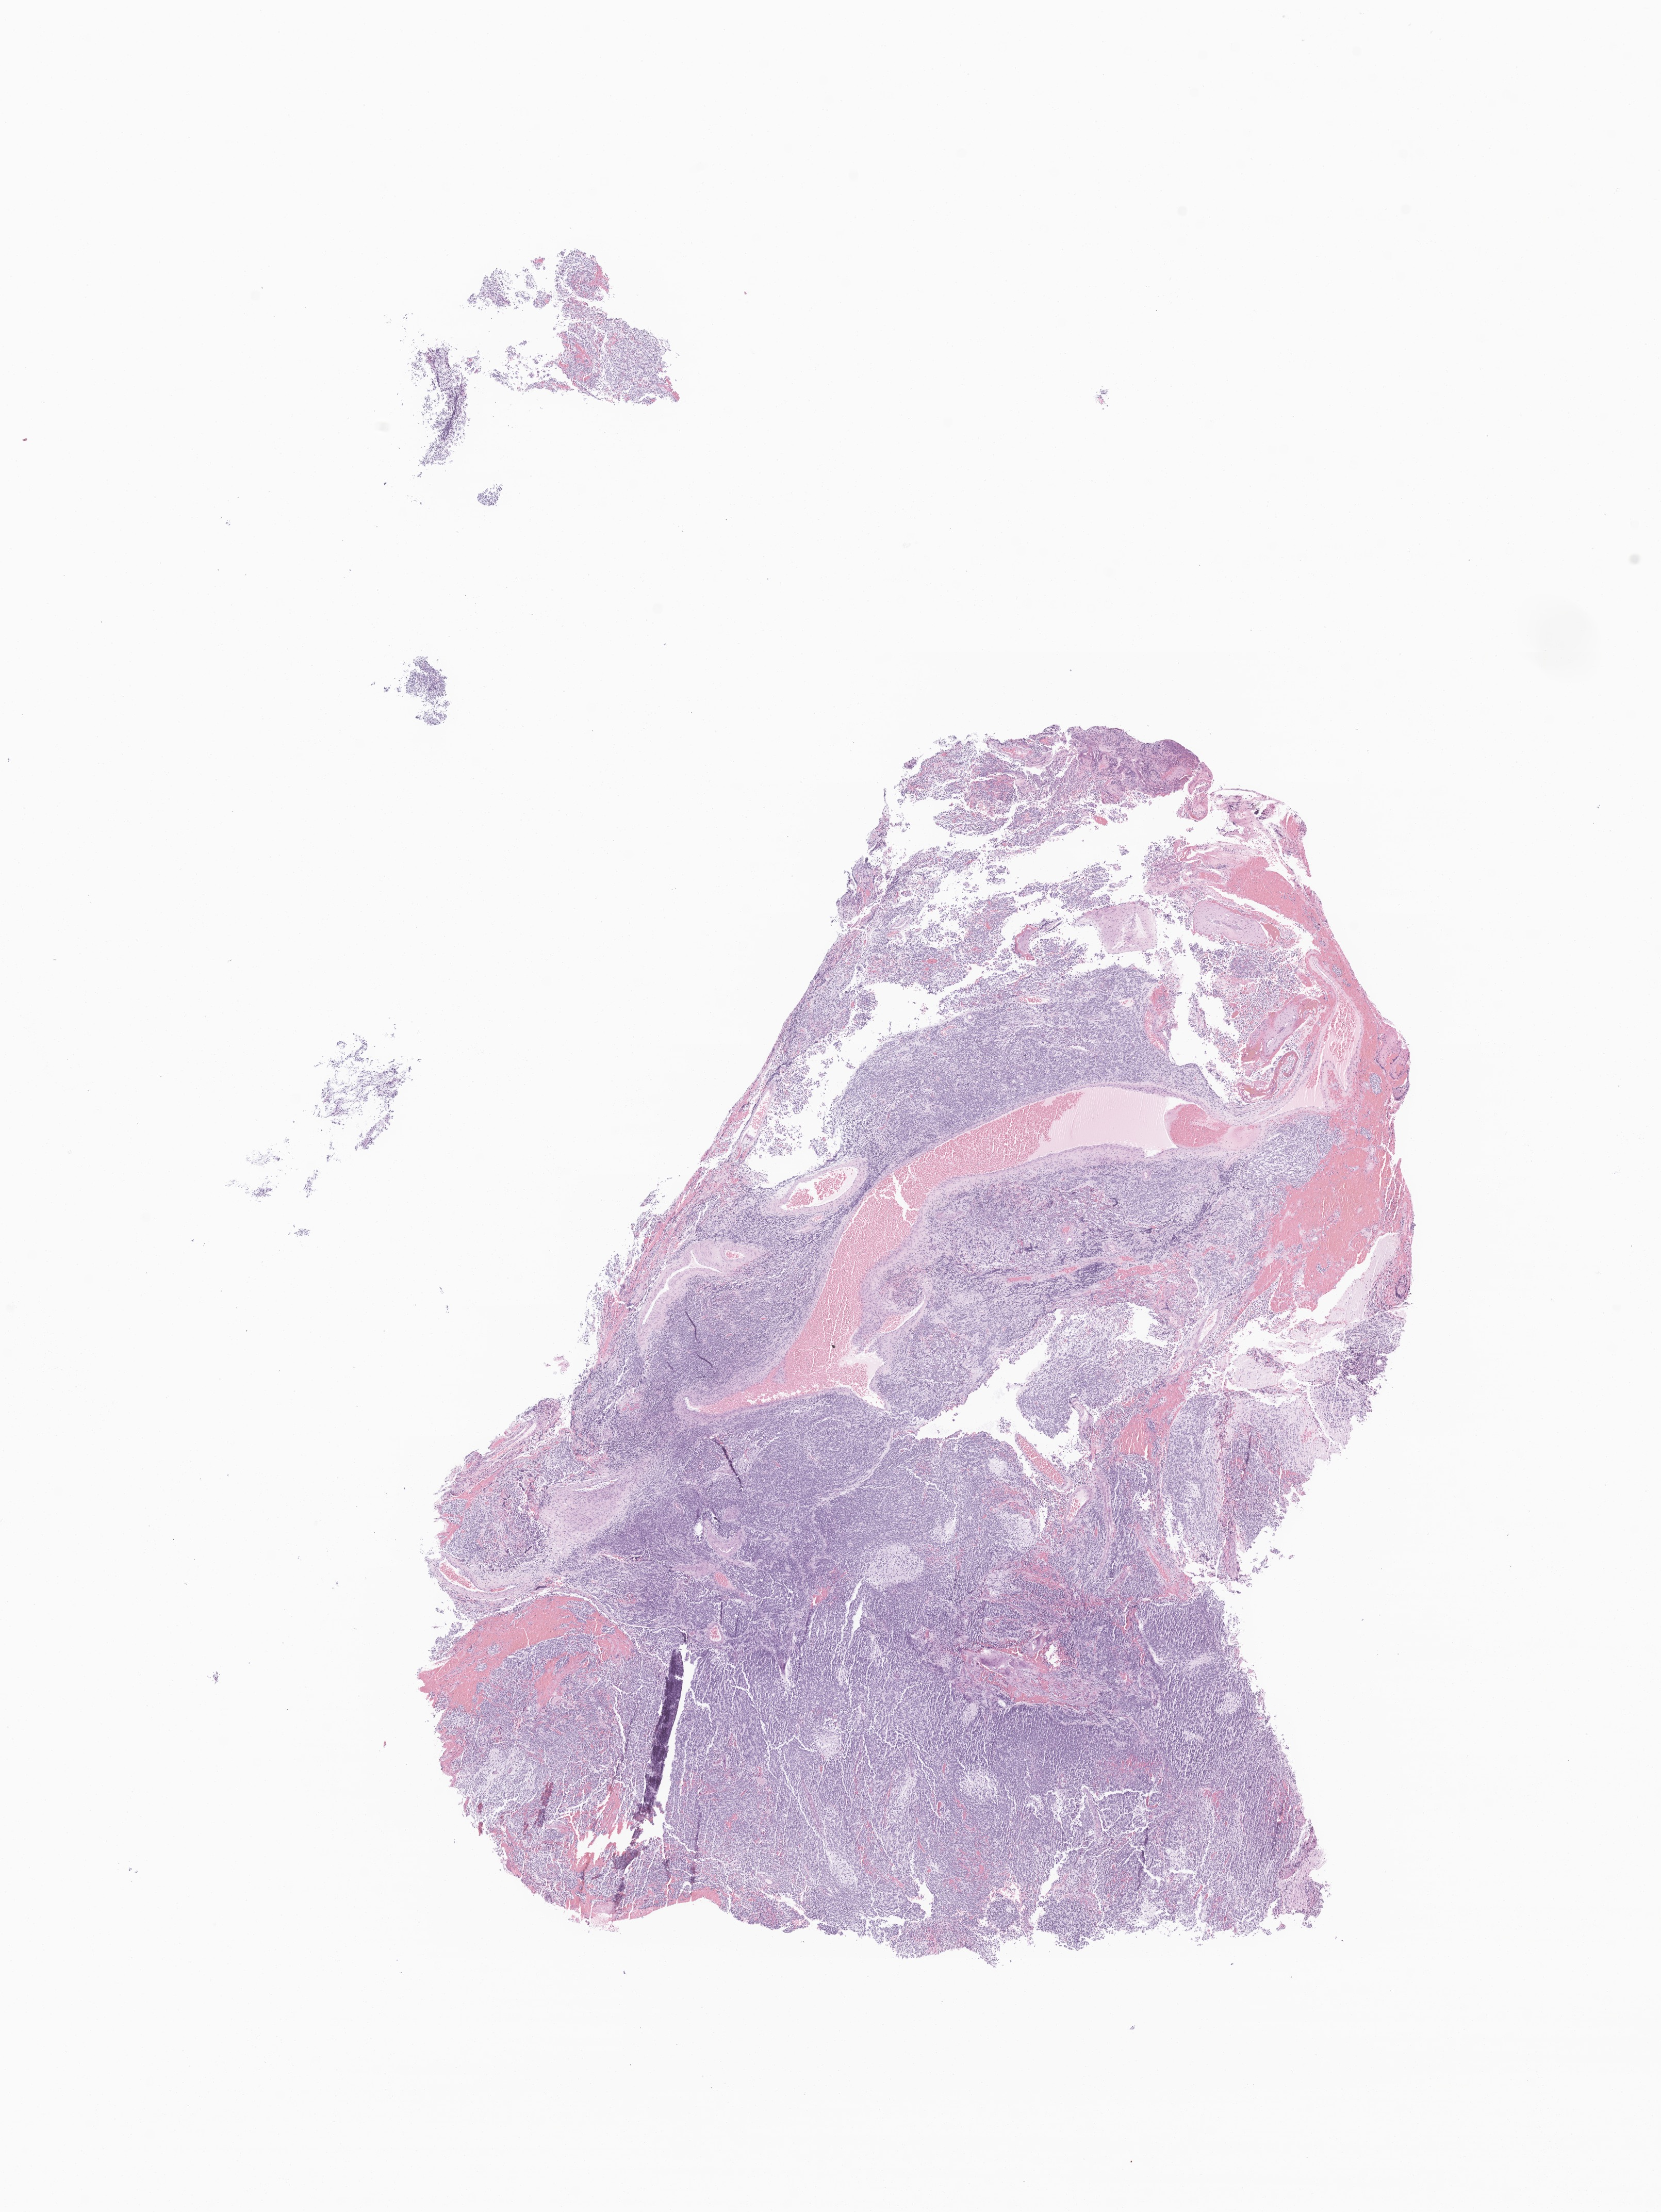
Digitized haematoxylin and eosin-stained section of tumor tissue from the cerebellum, a low-resolution overview of the entire scanned area, about 13.6 x 18.1 mm. FFPE section. Male patient, age 124 months.
• diagnosis: Medulloblastoma, NOS